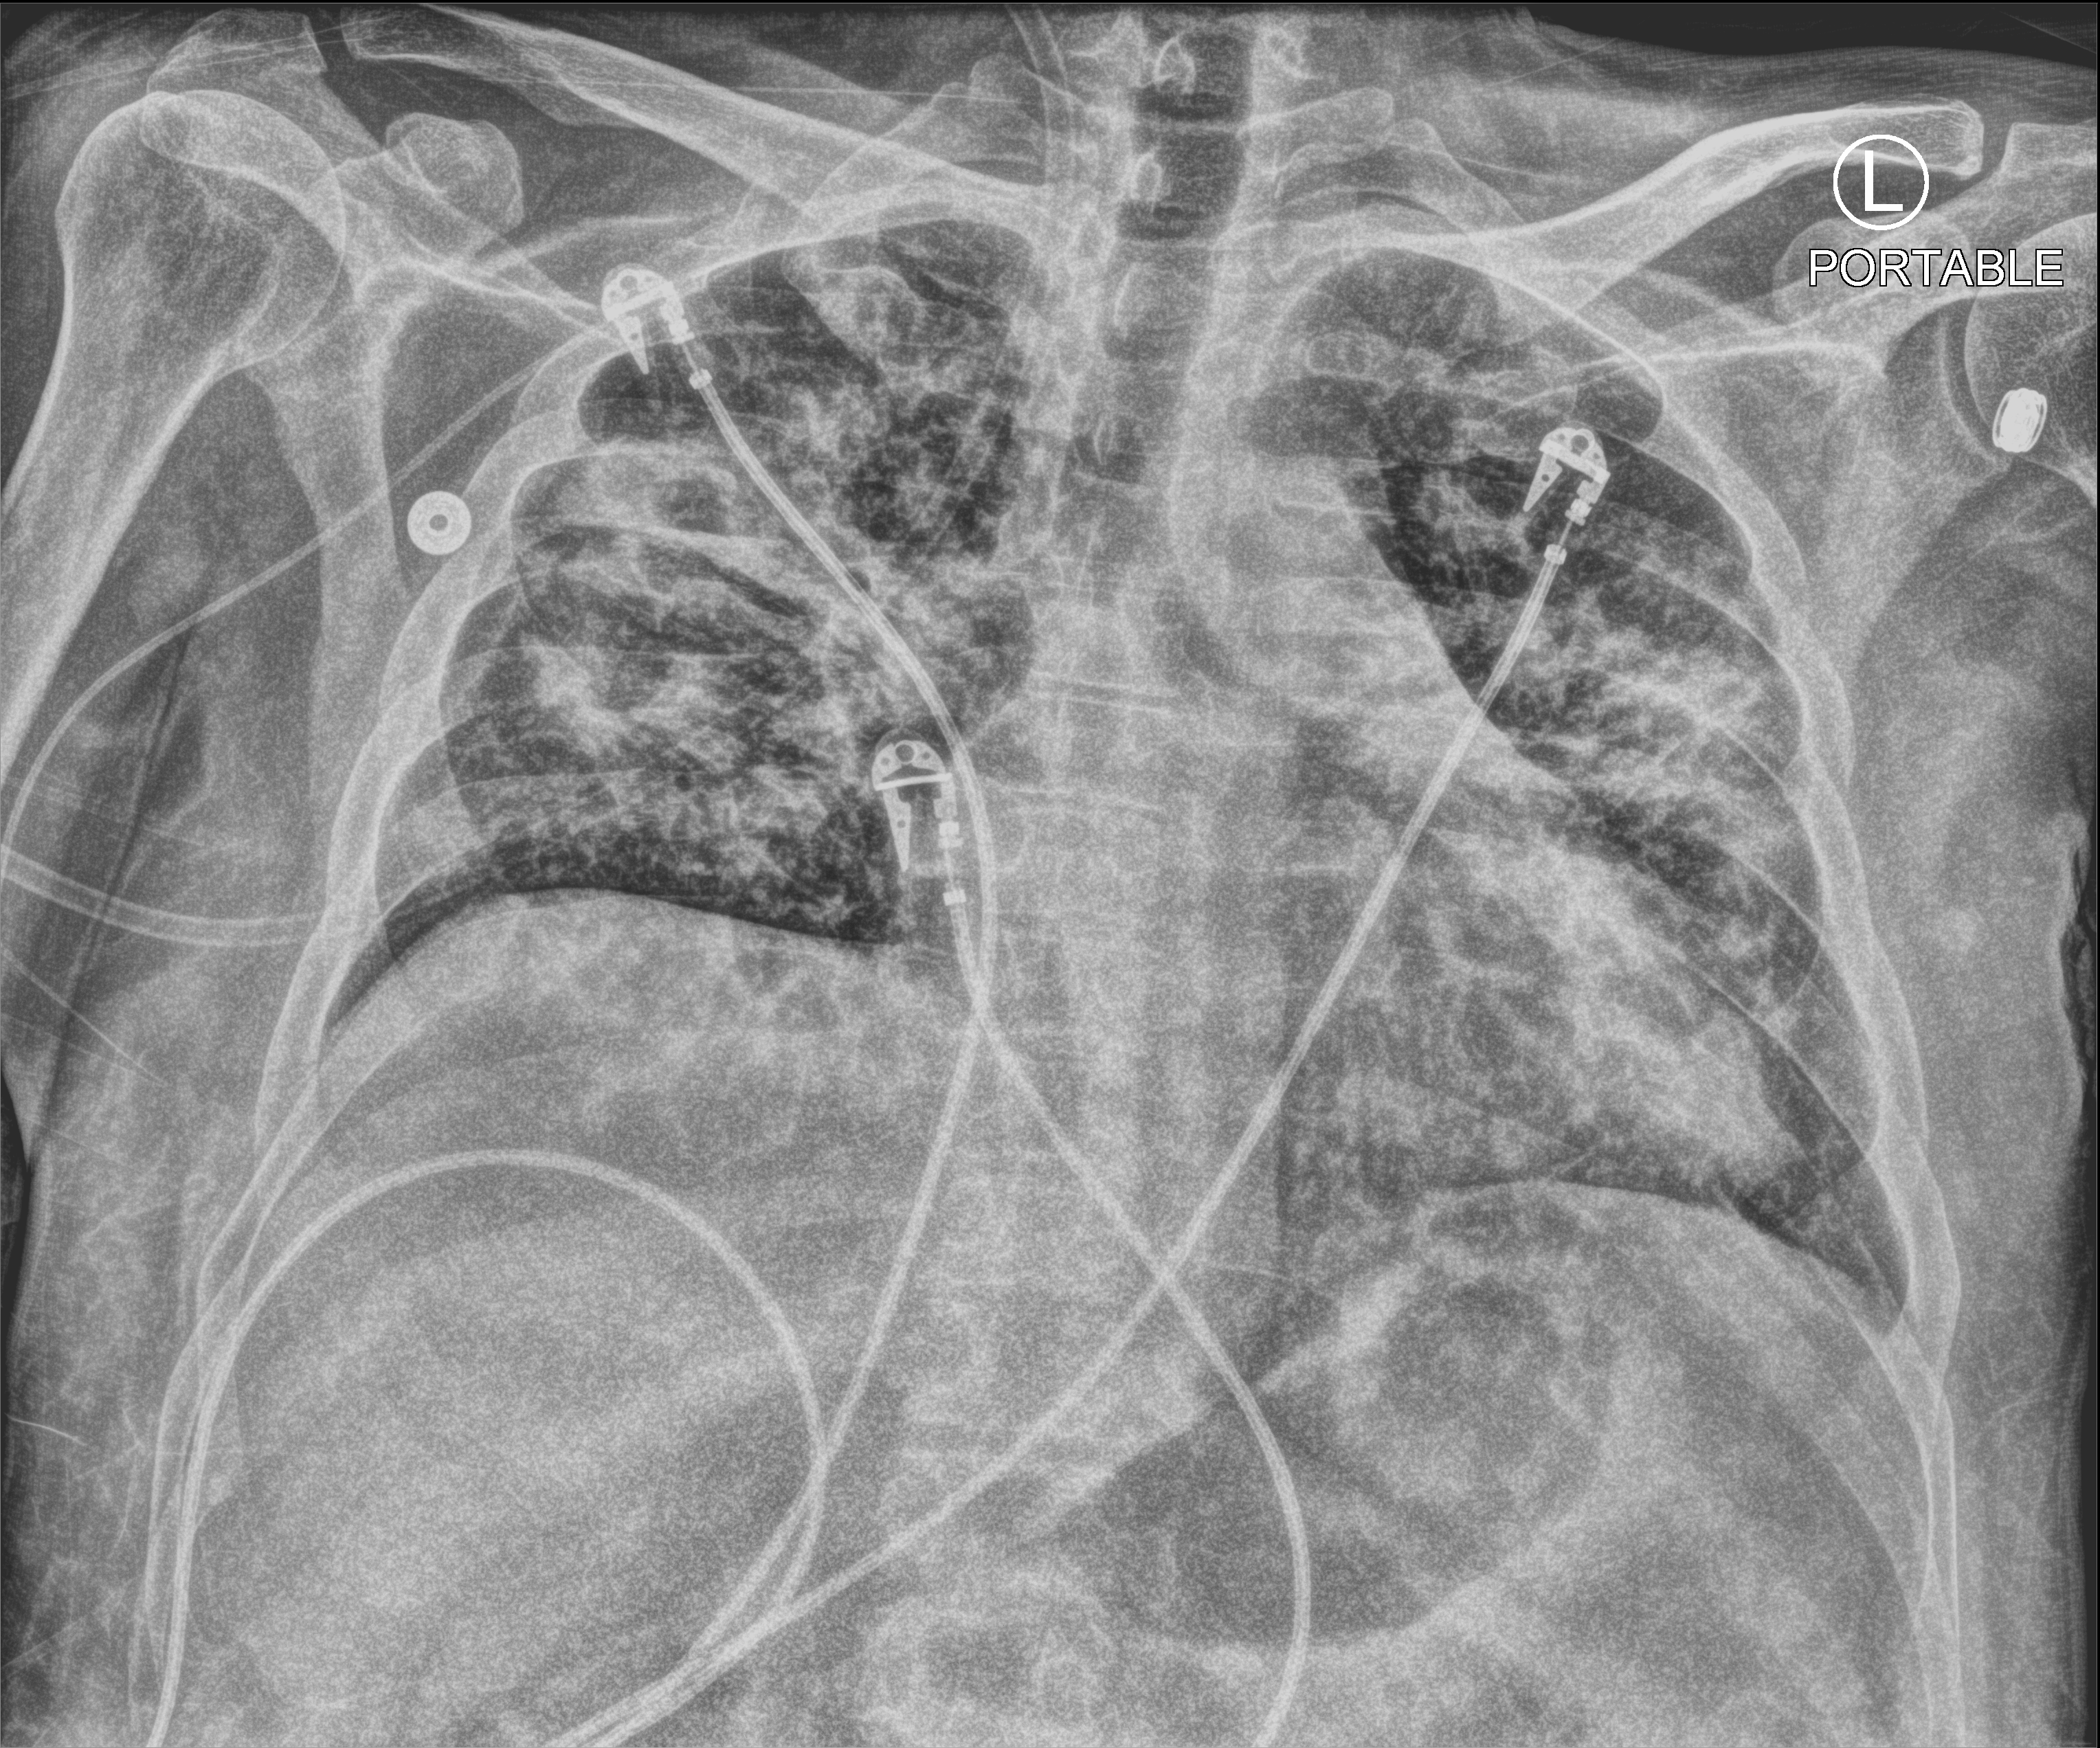
Portable chest radiograph, anteroposterior (AP) projection. Male patient hospitalised with COVID-19, age 18–59 years.
Hospital-stay facts (about this admission, not read from this image; timing relative to this image not recorded):
- smoking status (admission record): never